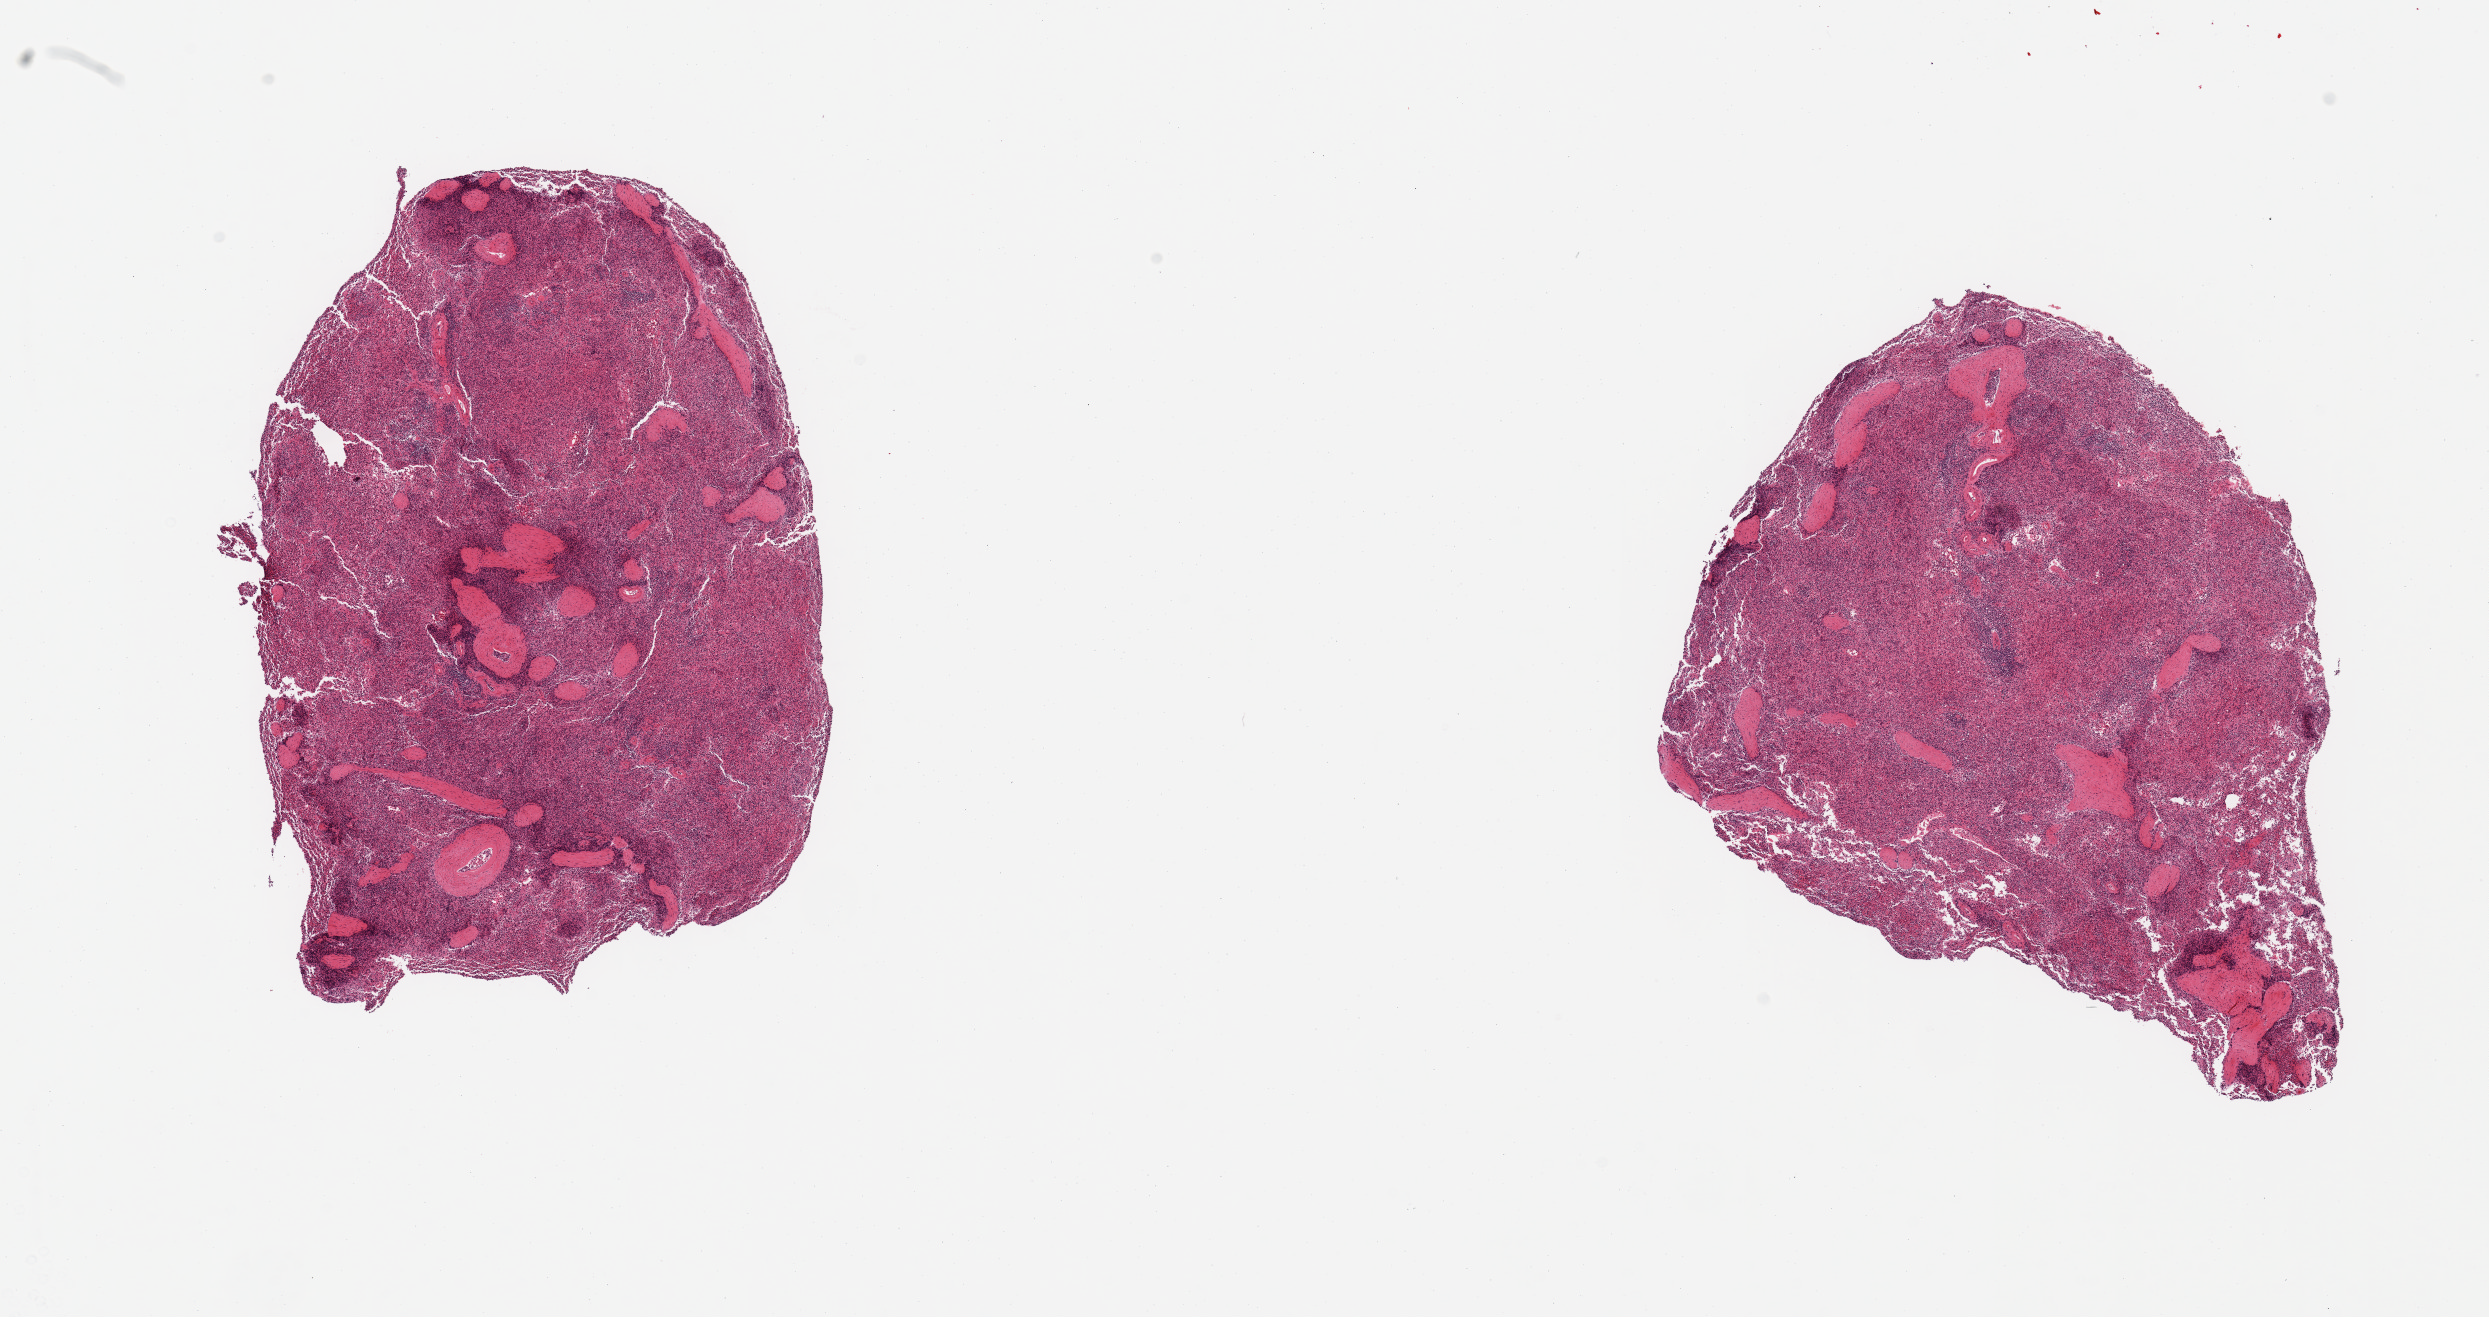
Whole-slide image, H&E stain, brightfield — shown as a low-resolution overview of the whole scanned area (about 19.7 x 10.4 mm). PAXgene-fixed paraffin-embedded (PFPE) section. Sampled site (target tissue): spleen. Tissue donor sample. Donor: male.
Review note (as recorded): 2 pieces, moderate-marked congerstion.